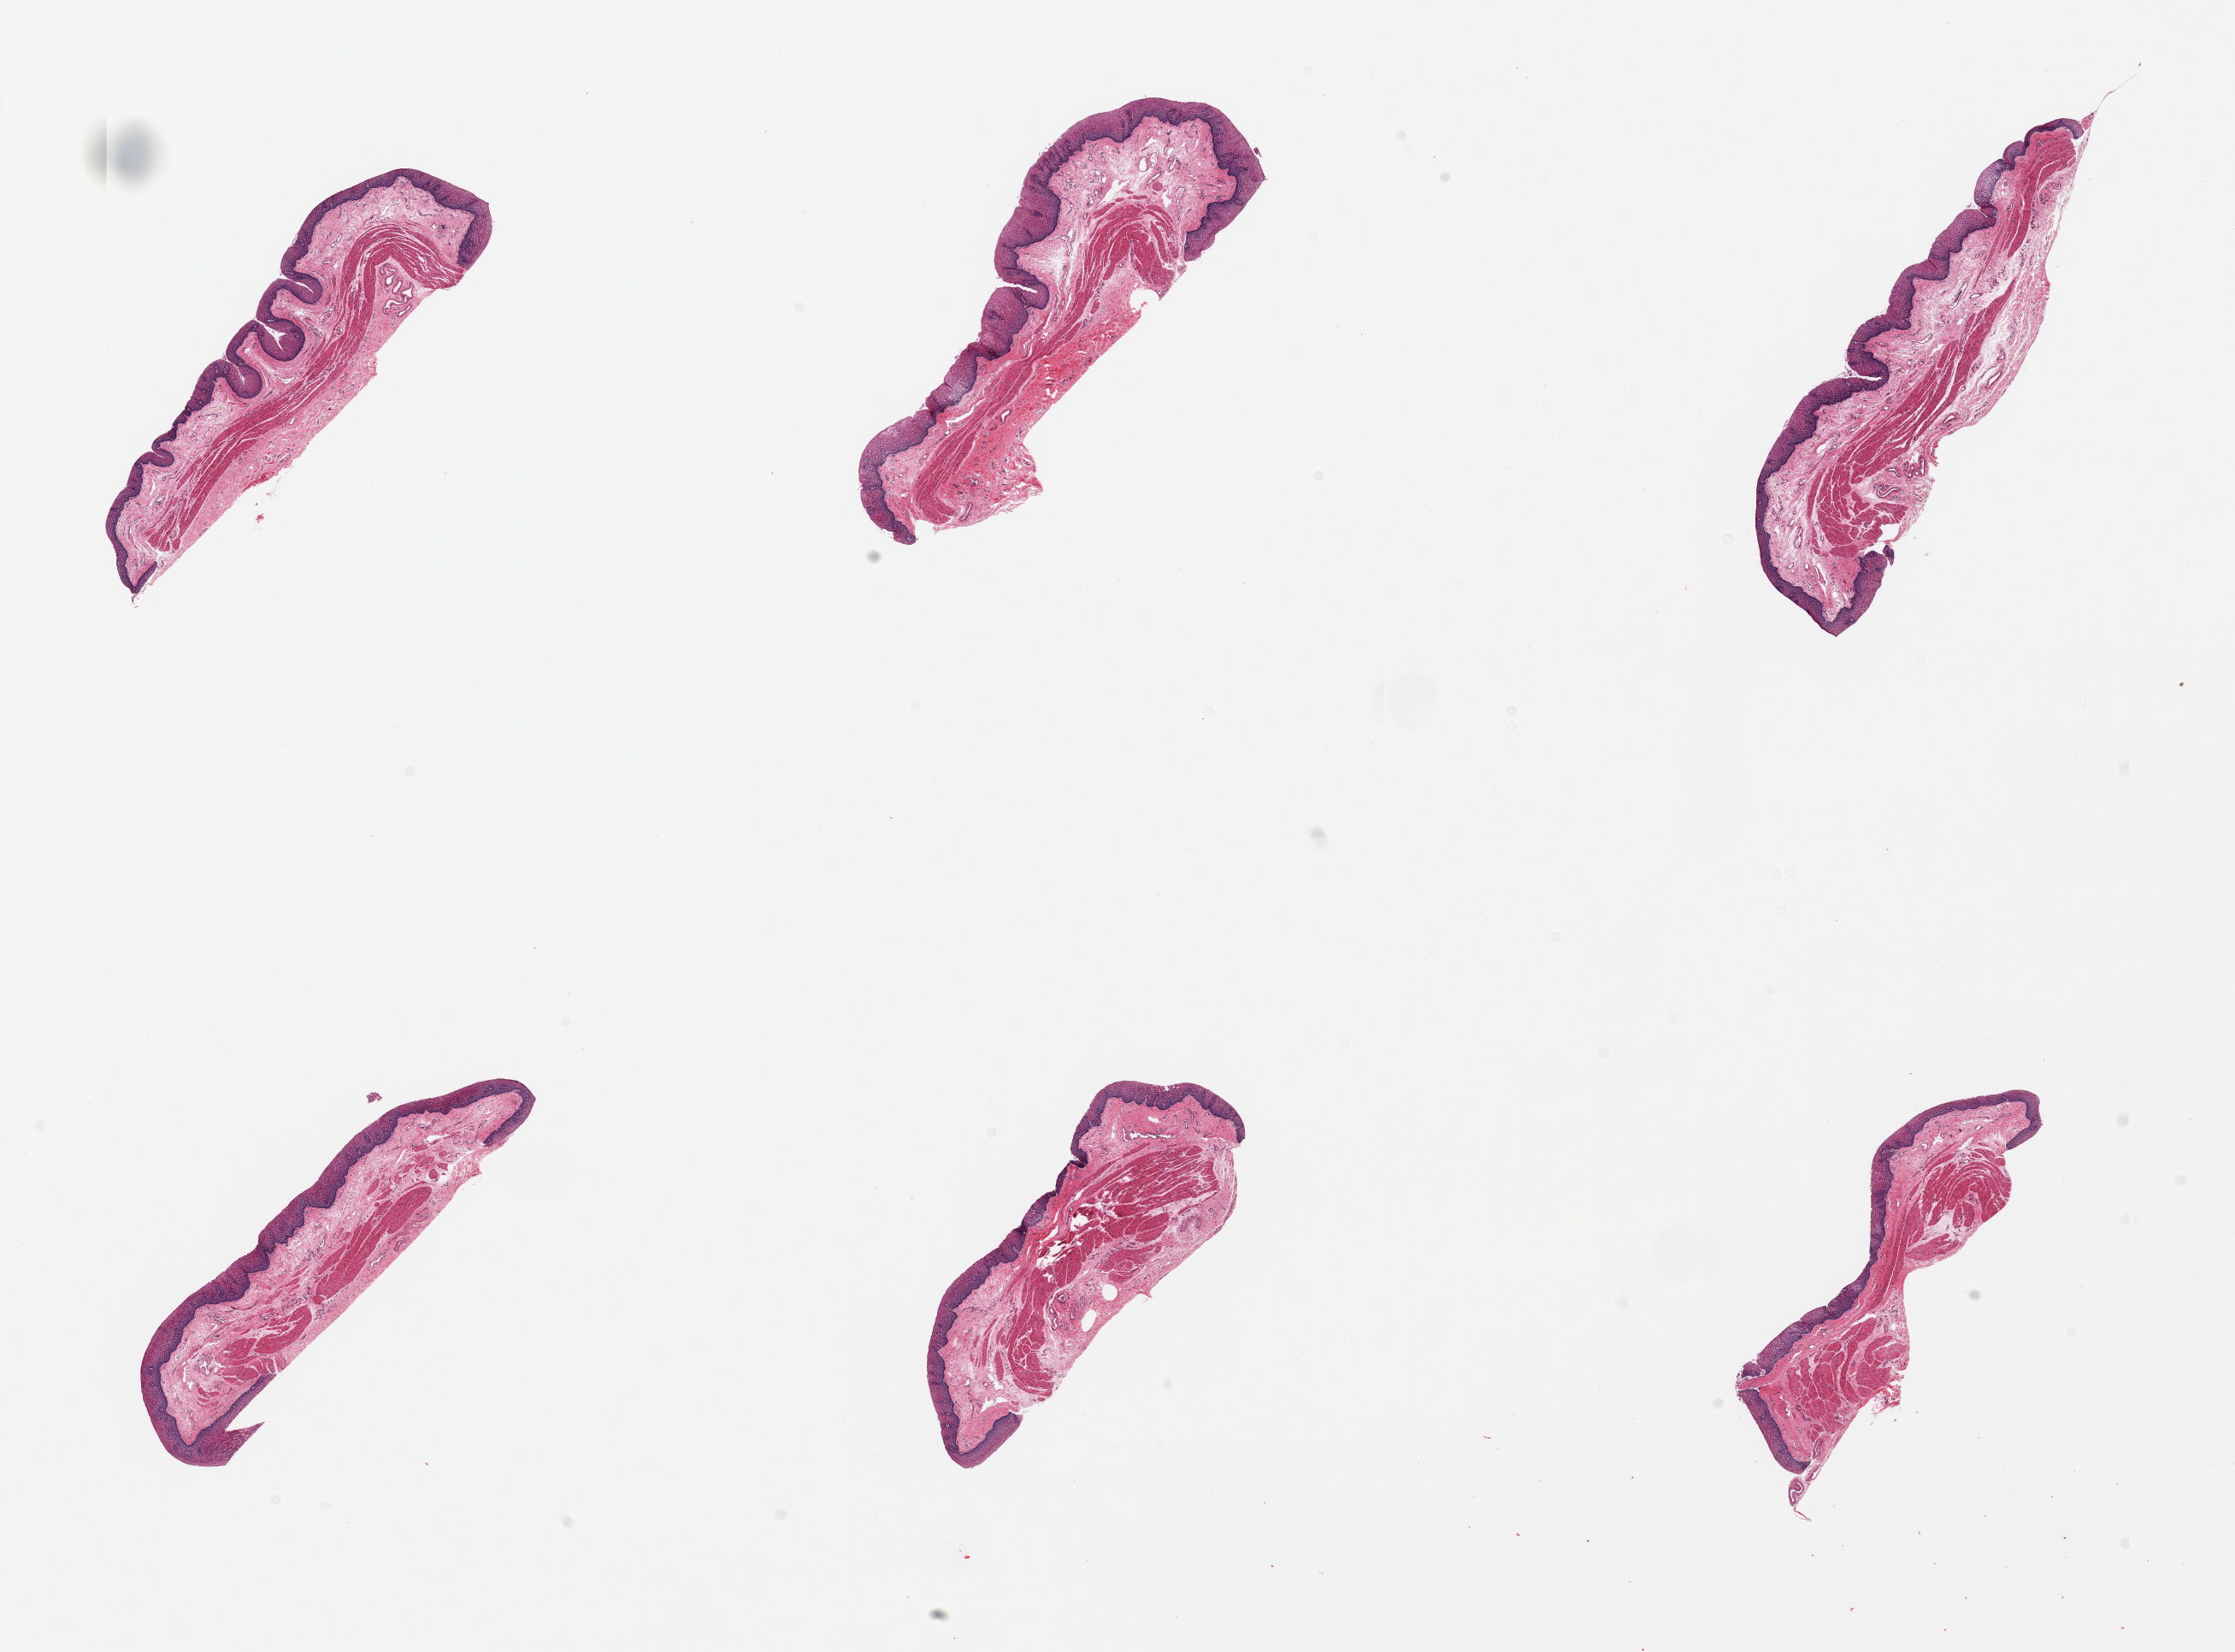
Haematoxylin and eosin whole-slide image, brightfield — a low-resolution overview of the entire scanned area, about 20.7 x 15.3 mm (slide scanned at 20x). PAXgene-fixed paraffin-embedded (PFPE) section. Section of esophageal mucous membrane (target tissue). Tissue donor sample. Donor sex: male.
• reviewer comment on this tissue sample: 6 pieces, squamous mucosa is ~0.15mm, ~10-15% thickness